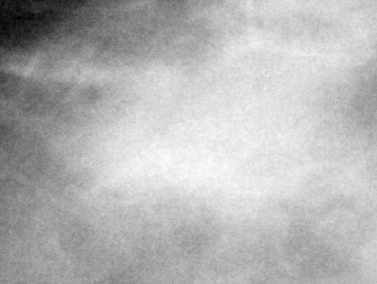
Cropped region of a digitized screen-film mammogram centred on a radiologist-marked abnormality, right breast, MLO view, BI-RADS breast density category 3 (scale 1–4).
Mass, shape irregular / architectural distortion, margins obscured / spiculated; BI-RADS assessment category 4; pathology (as recorded): malignant.